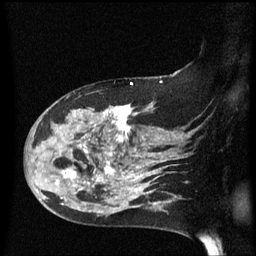
Breast MRI (dynamic contrast-enhanced), one sagittal slice. Slice 40 of 60 in the series (ordered by position). Dynamic contrast-enhanced series, image 2 of 3 at this slice position (ordered by acquisition). 1.5 T. TE 4.2 ms, TR 8.4 ms. 256 × 256 image matrix. Female patient, age 47 years.
Outlined on this slice (semi-automatic segmentation, software-assisted and operator-edited):
- analysis volume of interest (the breast-tissue region the enhancement analysis was run in; not a lesion): box from (x=24, y=97) to (x=149, y=206) px
- tumour enhancement mask (voxels above the 70 % enhancement threshold inside the analysis volume of interest): (x=56, y=105)–(x=149, y=200)